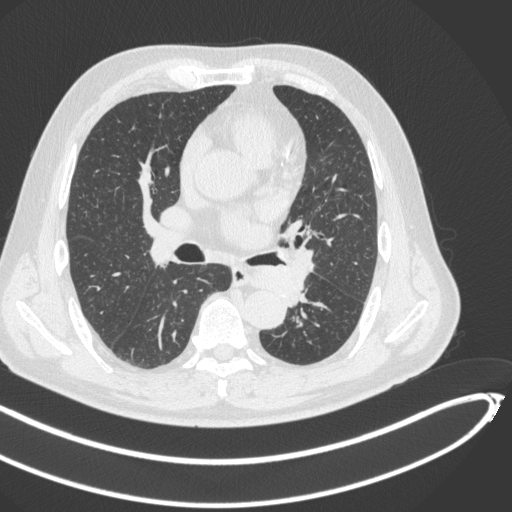
Chest CT, one axial slice. Slice 256 of 466 in the series (ordered by position). 120 kVp. Lung window (W 1500 / L -600 HU). 1 mm slice thickness. 512 × 512 image matrix, field of view 400 × 400 mm. Patient: male, 64 years. From the clinical record (not read from this slice): clinical TNM (as recorded): T1c N0 M0; histopathological grade: G2.
Structures marked on this image (rectangle marked by the reading radiologist):
- lung tumour (recorded histology: squamous cell carcinoma): bounding box <238,261,311,309> (left, top, right, bottom; pixels)